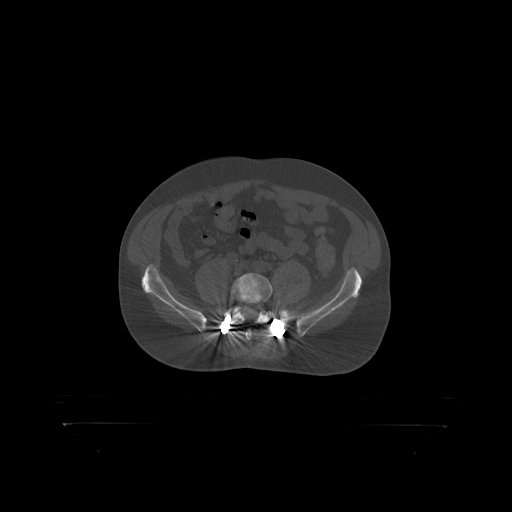
CT including the spine, one axial slice. Position 198 of 399 along the scan axis. Bone window (W 1800 / L 400 HU). 512 × 512 image matrix, field of view 650 × 650 mm. Male patient, age 46 years. Case-level facts recorded for this patient, not image findings: primary cancer: skin.
Outlined on this slice (semi-automatically segmented with operator editing):
- L5 vertebra: box from (x=231, y=273) to (x=273, y=319) px